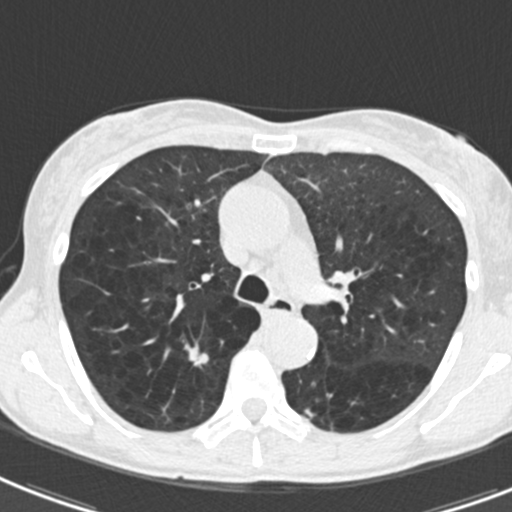
Chest CT (low-dose screening protocol), one axial image, second screening round (one year after baseline), lung window (W 1500 / L -600 HU), slice 58 of 186 in the series. Female participant, aged 61 years at enrolment. Current smoker at enrolment.
• Lesion marked by an expert reader, bounding box <170,333,224,379> (left, top, right, bottom; pixels).
• Screening reader's record for this exam (one nodule recorded; not confirmed to be the boxed lesion): non-calcified nodule or mass ≥4 mm, right upper lobe, 12 × 6 mm, smooth margins, soft tissue attenuation, pre-existing on the prior screen: yes; interval growth: yes.
• Official screen result: positive, change unspecified: nodule(s) >= 4 mm or enlarging nodule(s), mass(es), or other non-specific abnormalities suspicious for lung cancer.